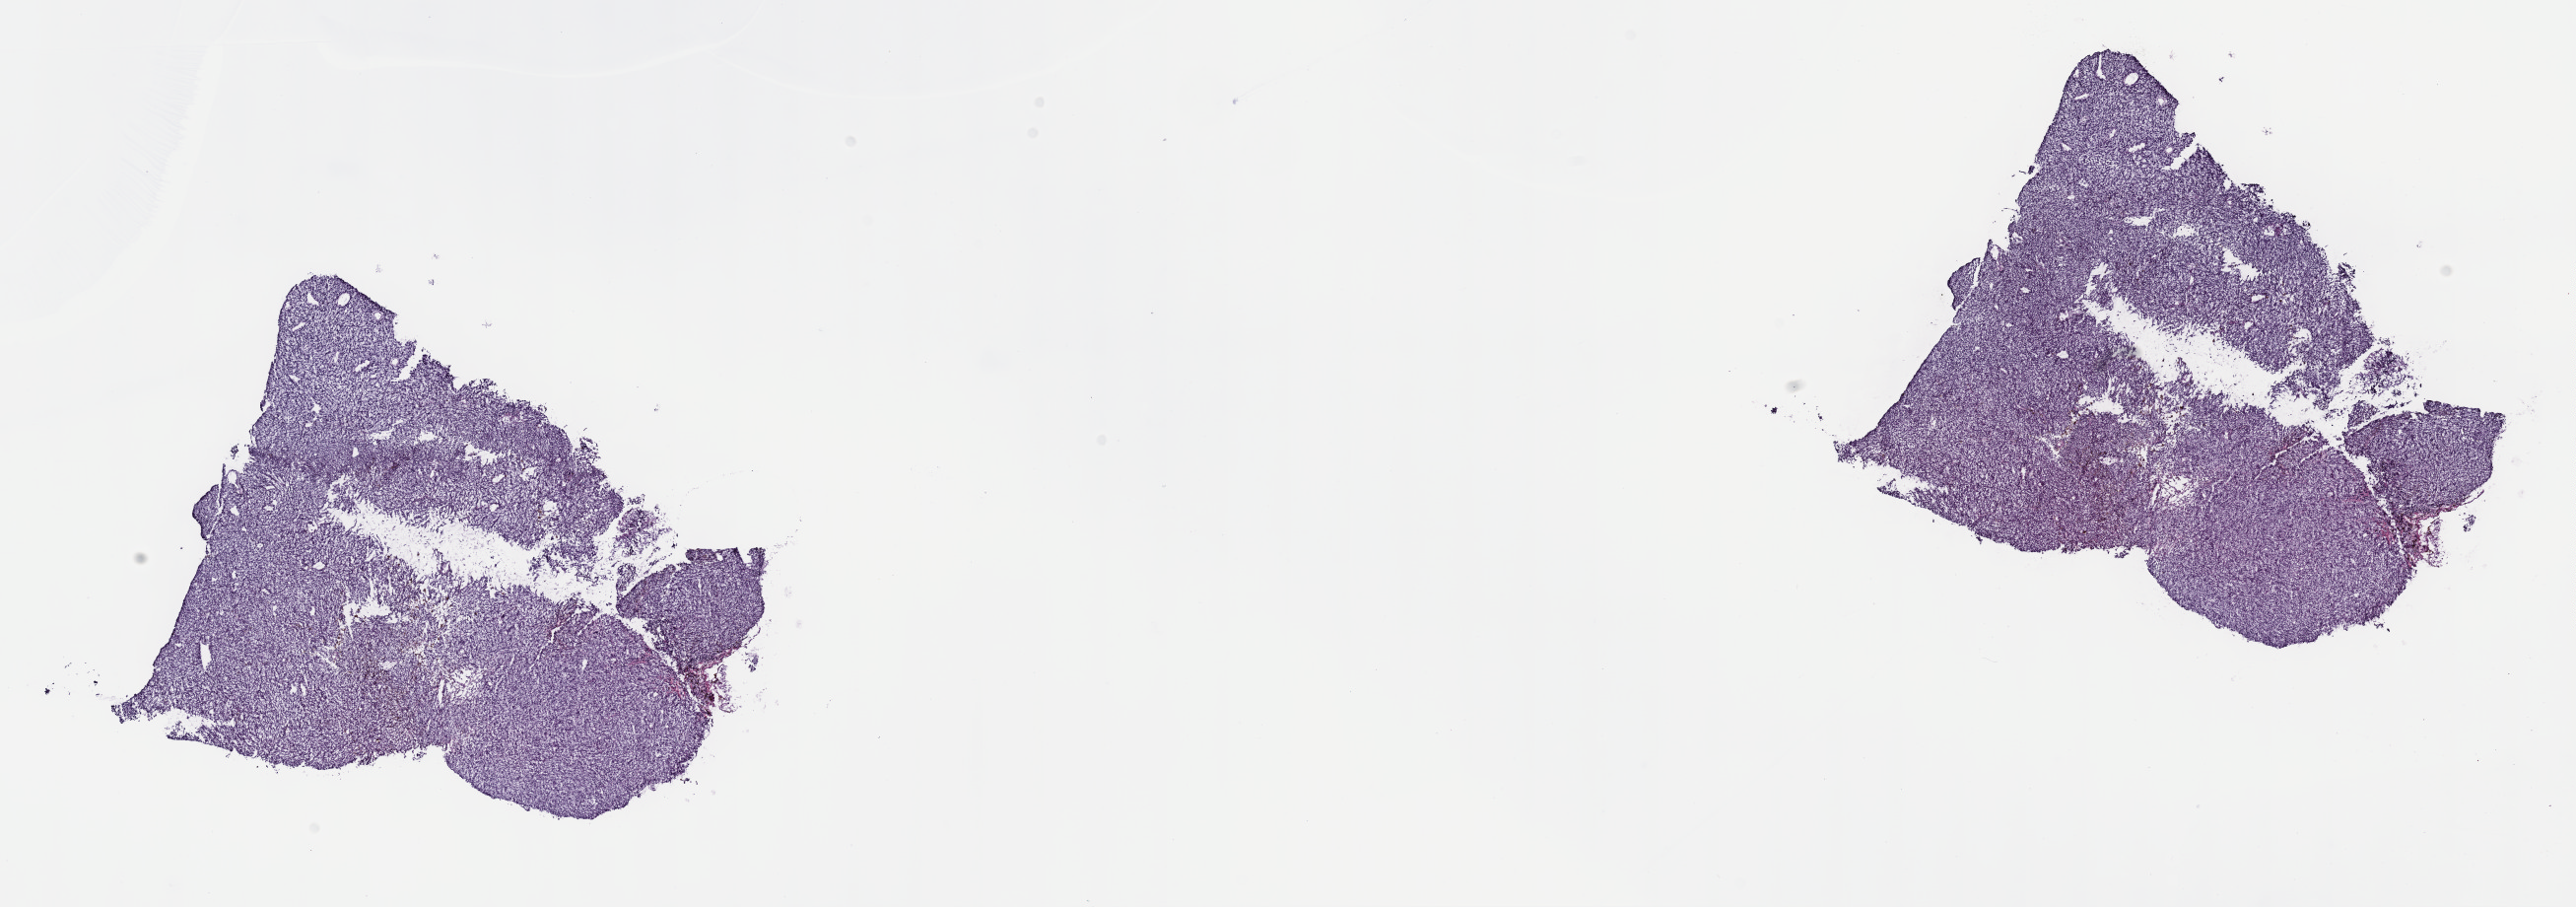
H&E-stained whole-slide image — whole scanned area (about 21.1 x 7.4 mm, acquisition: 40x scan) shown as a low-resolution overview; frozen section from the top of the tissue portion; primary tumour sample from the uvea. Female patient; age at initial diagnosis 44 years. Pathologist review of this section (percent, as recorded): tumour cells 100%, tumour nuclei 80%, normal cells 0%, stromal cells 0%, necrosis 0%. Inflammatory infiltration, as recorded: lymphocyte infiltration 1%, monocyte infiltration 0%, neutrophil infiltration 0%.
* laterality: left
* AJCC pathologic stage: IIIA
* histologic diagnosis: Mixed epithelioid and spindle cell melanoma (choroid)